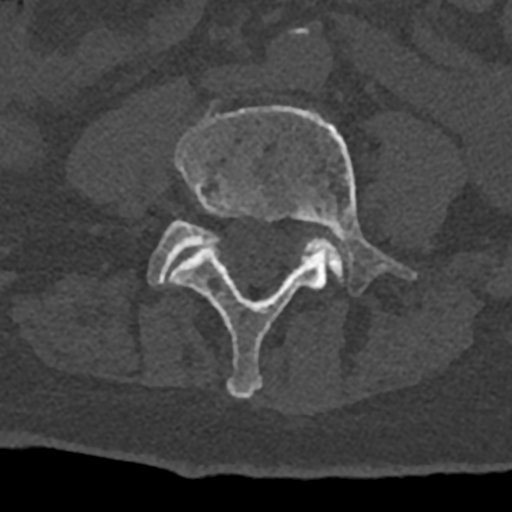
CT including the spine, one axial slice. Position 245 of 797 along the scan axis. Reconstruction kernel Br40s/3. Bone window (W 1800 / L 400 HU). 0.5 mm slice thickness. 512 × 512 image matrix, field of view 160 × 160 mm. Male patient, age 74 years. Case-level facts recorded for this patient, not image findings: primary cancer: renal; vertebrae with lytic lesions (as recorded): T10, L1, L2, L3, L4, L5.
Structures marked on this image (semi-automatic segmentation, software-assisted and operator-edited):
- L4 vertebra: bounding box <169,105,417,399> (left, top, right, bottom; pixels)
- L5 vertebra: <148,221,342,286>